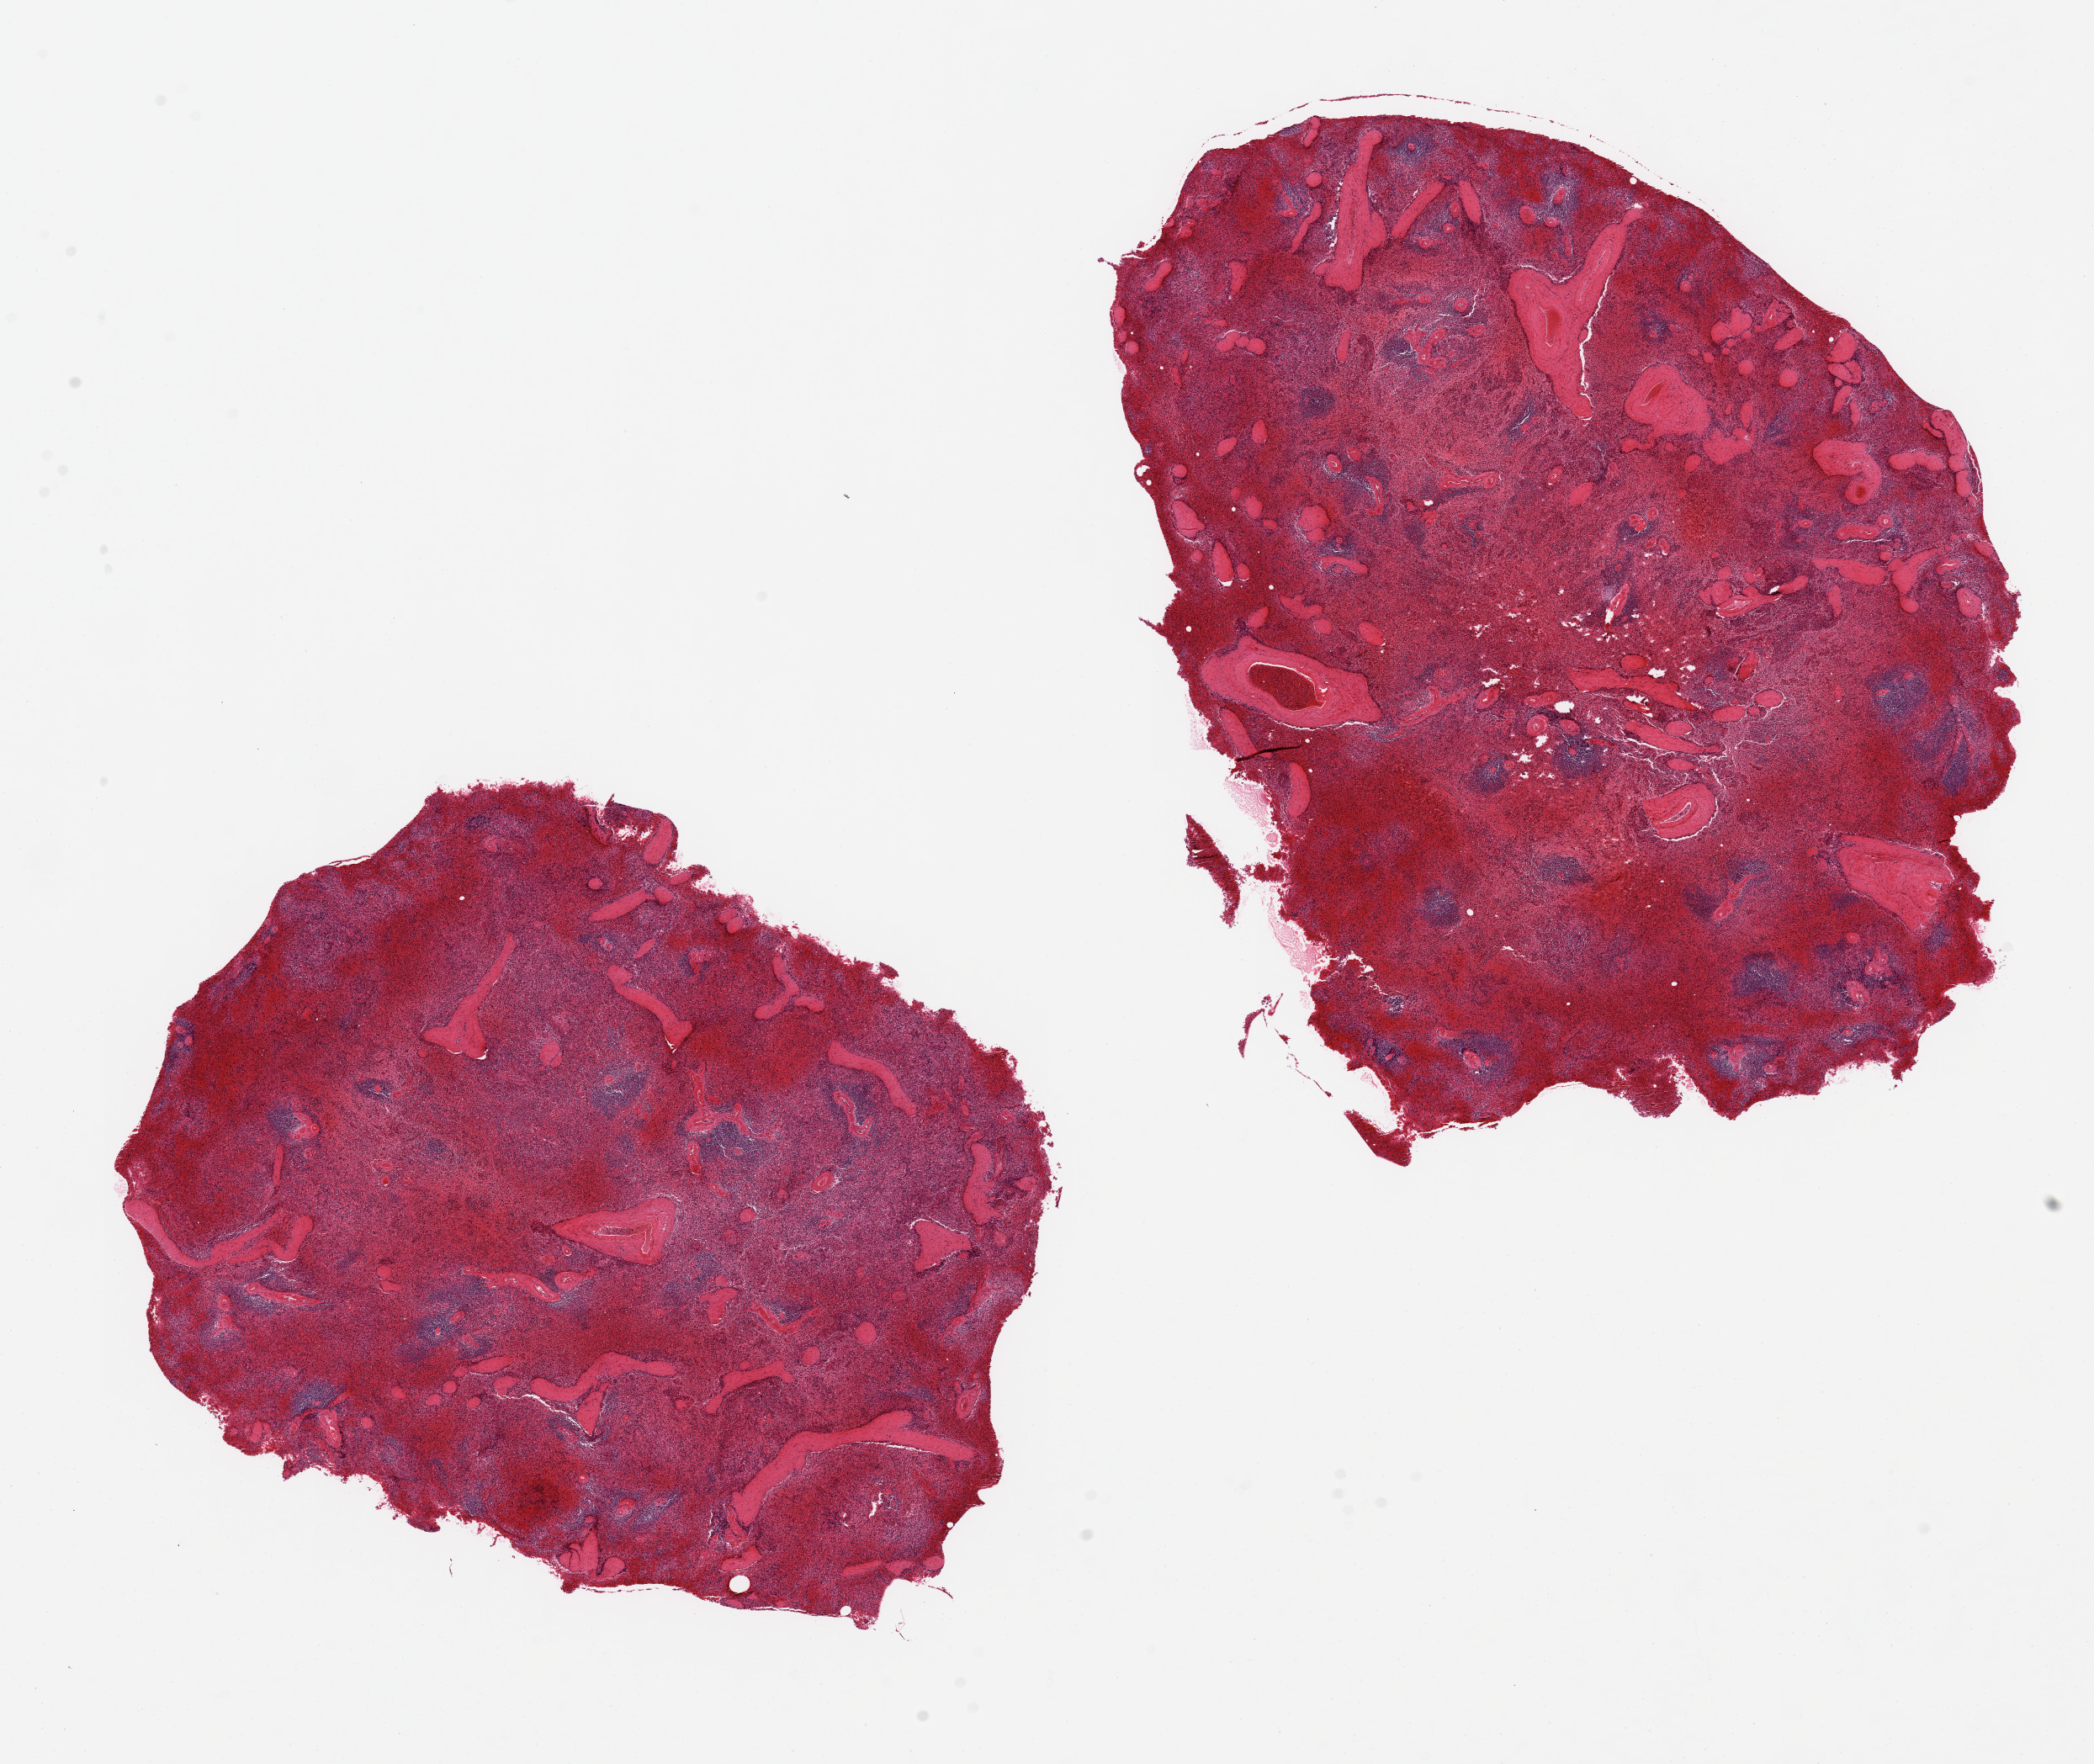
Hematoxylin and eosin (H&E) whole-slide image — low-resolution overview of the scanned area, about 19.7 x 16.6 mm; PAXgene-fixed paraffin-embedded (PFPE) section; target tissue: spleen; donor tissue sample. Male donor.
Review note (as recorded): 2 pieces, marked congestion.